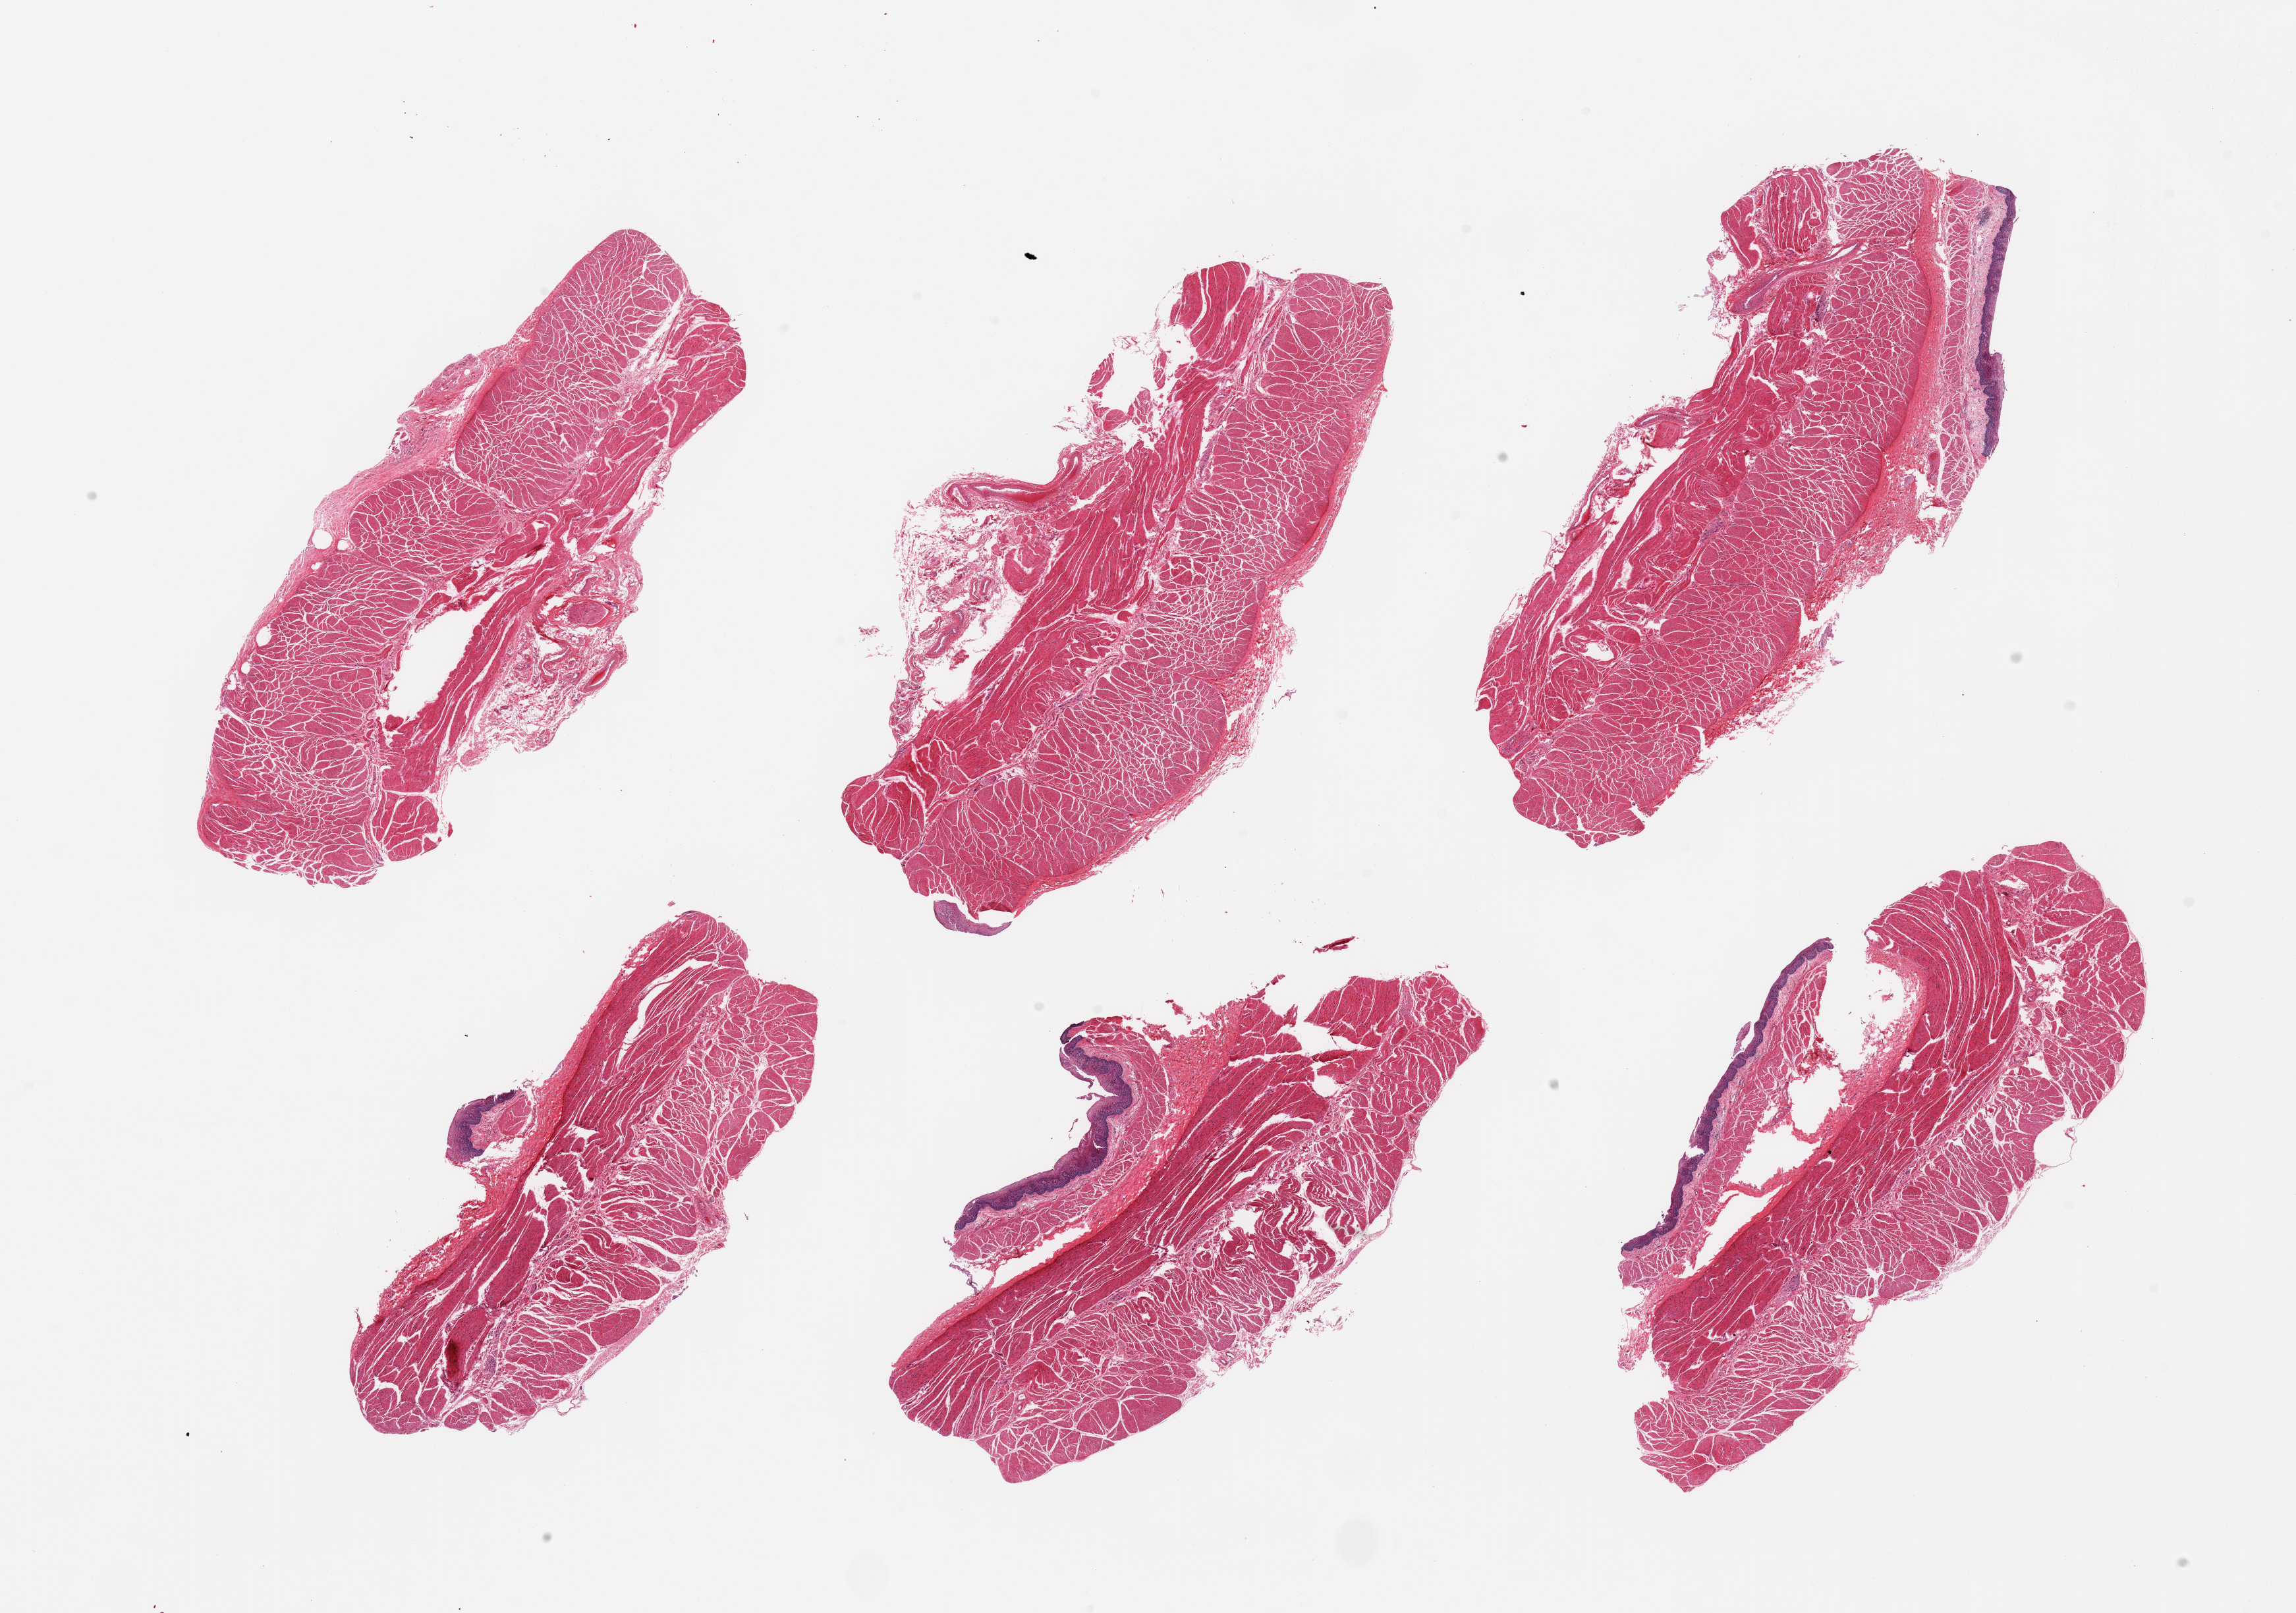
Whole-slide image, hematoxylin and eosin (H&E) stain — shown as a low-resolution overview of the whole scanned area (about 27.6 x 19.4 mm). PAXgene-fixed, paraffin-embedded tissue. Target tissue: esophageal muscle. Donor tissue sample. Donor sex: male.
Reviewer comment on this tissue sample: 6 pieces, confirmed target muscularis; trace 'contaminant squamous mcuosa, ~5-10% total.